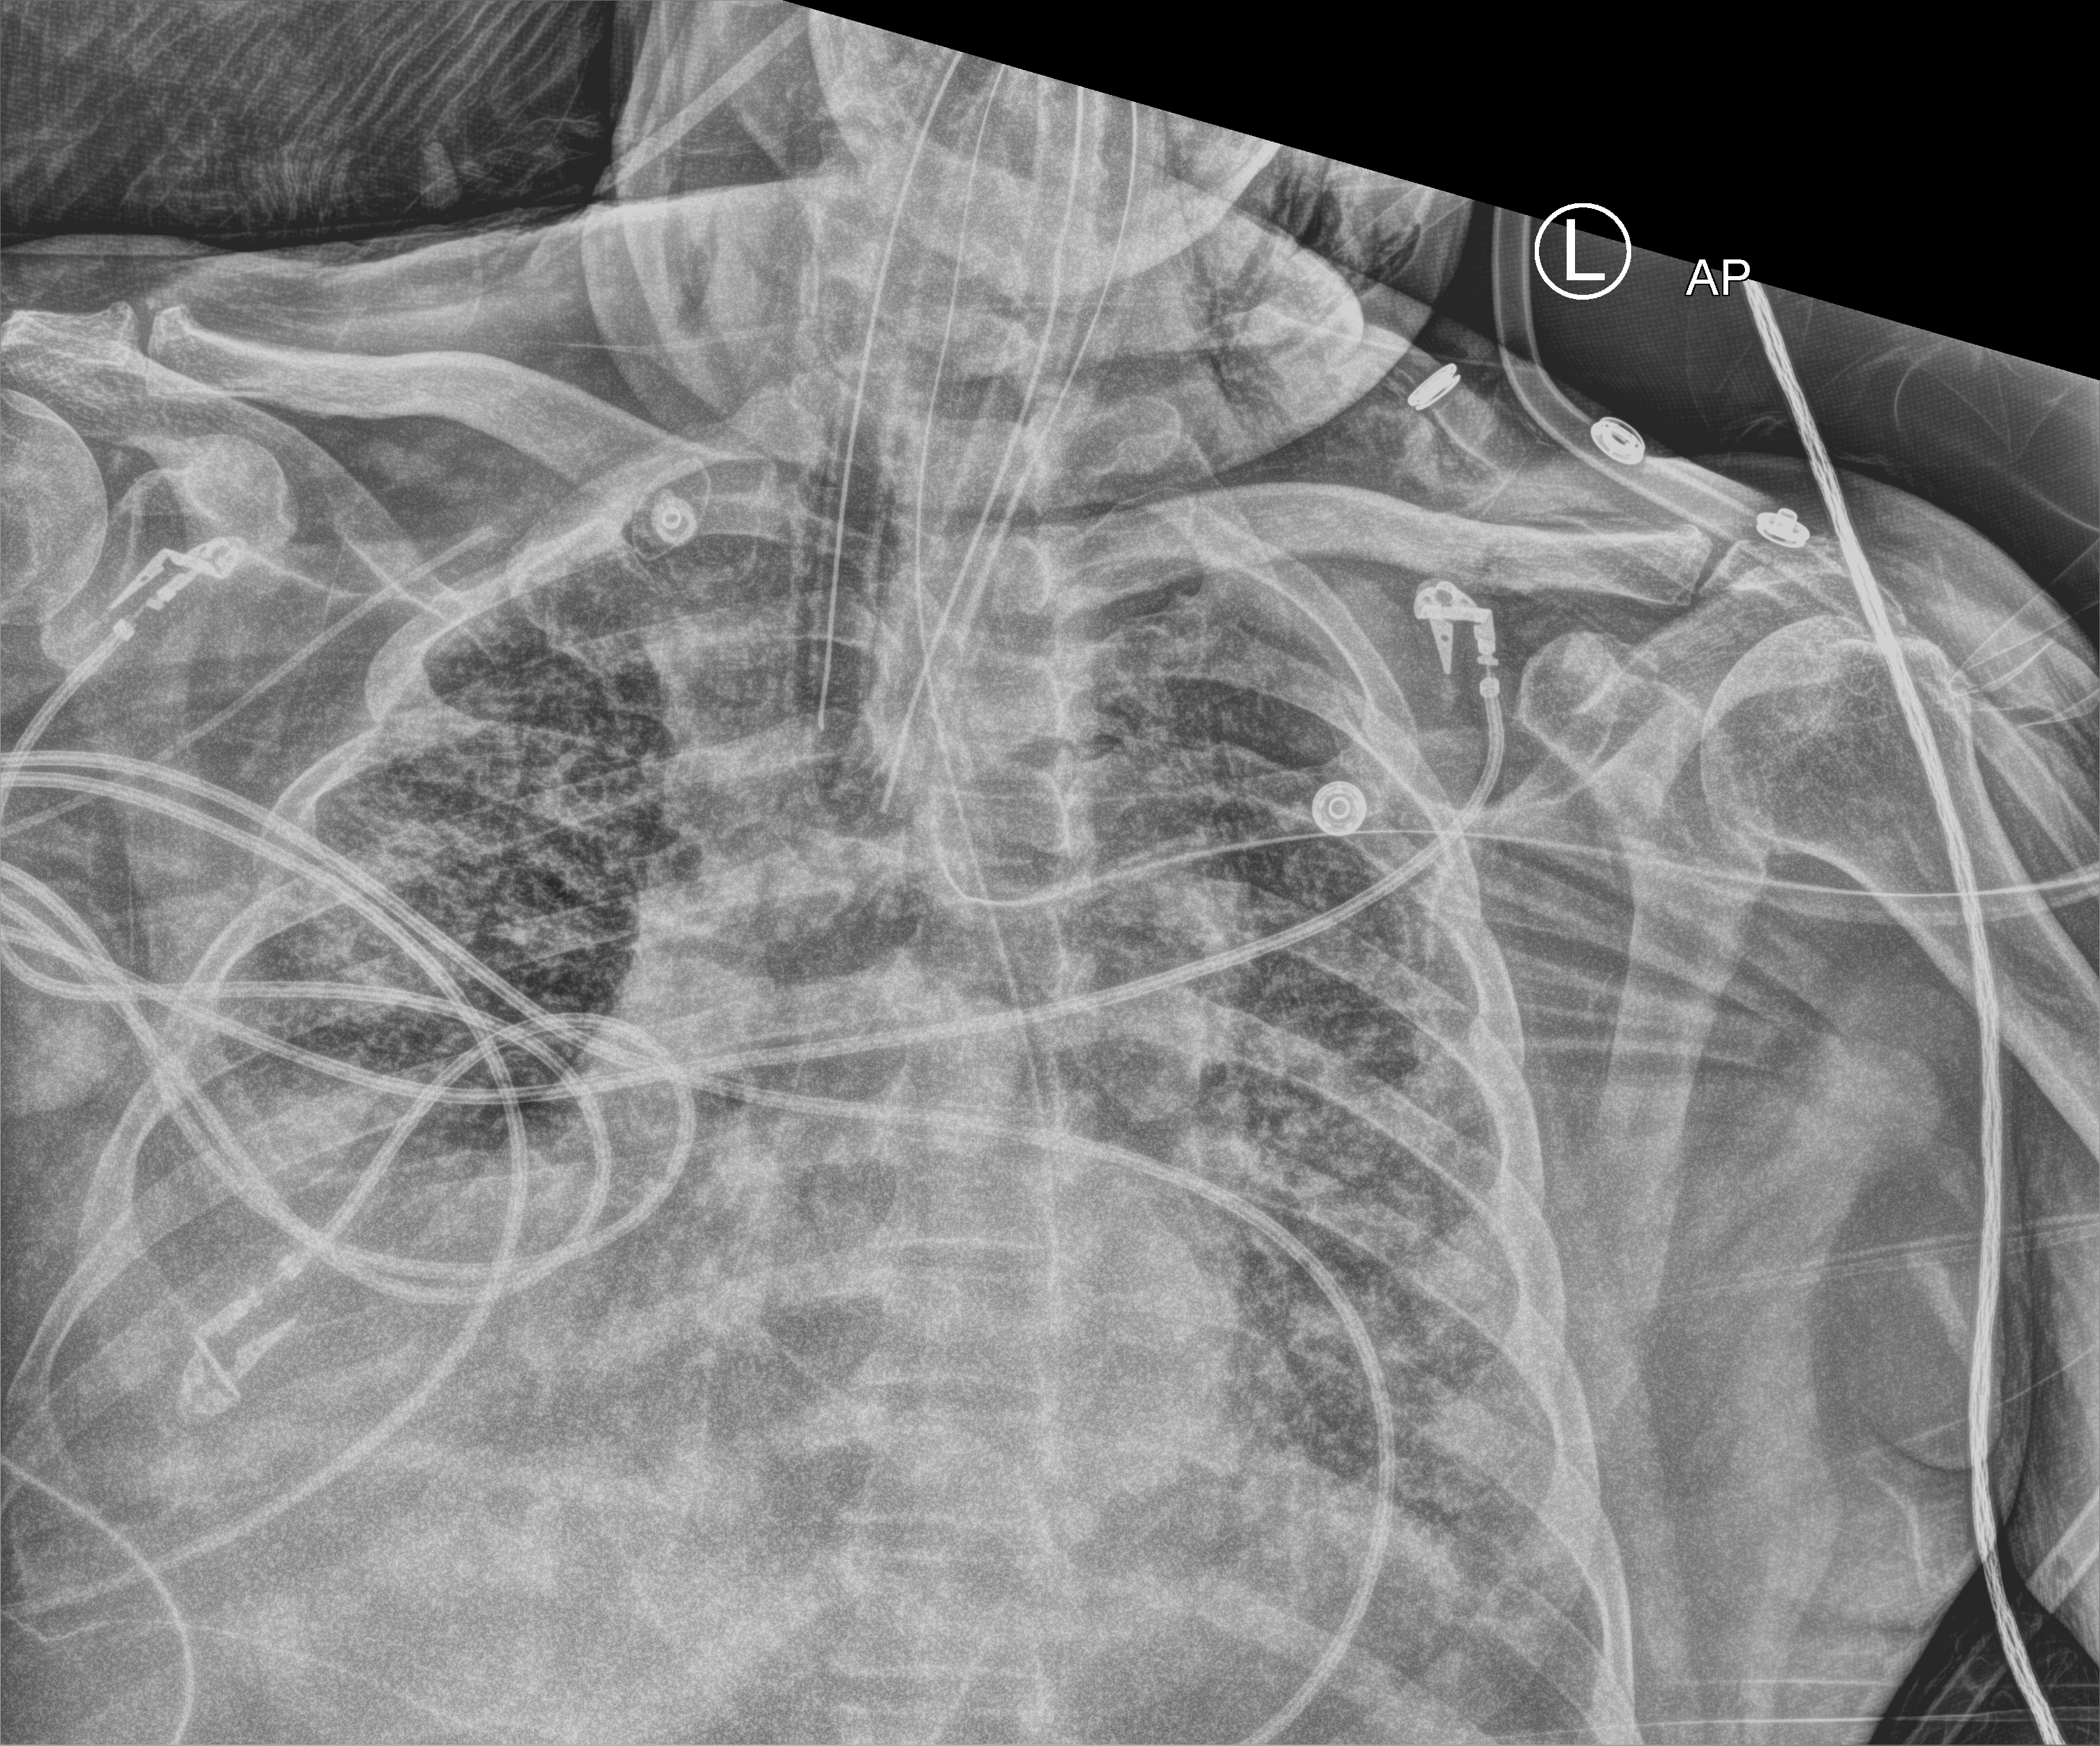
Portable chest radiograph; anteroposterior (AP) projection. Patient hospitalised with COVID-19; male, aged 60–74 years.
From the hospital-stay record, not from the radiograph (when in the stay this image was taken is not recorded): length of hospital stay: 26 days; chronic kidney disease (admission record): no; admitted to intensive care during this hospital stay: yes.